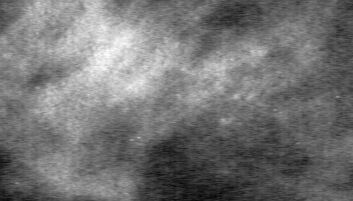
Cropped region of a digitized screen-film mammogram centred on a radiologist-marked abnormality, left breast, MLO view, BI-RADS breast density category 2 (scale 1–4).
Marked abnormality: calcifications, morphology pleomorphic, distribution clustered; BI-RADS assessment category 4; subtlety rating 2 on a 1 (subtle) to 5 (obvious) scale; pathology result (as recorded, not read from the image): benign.